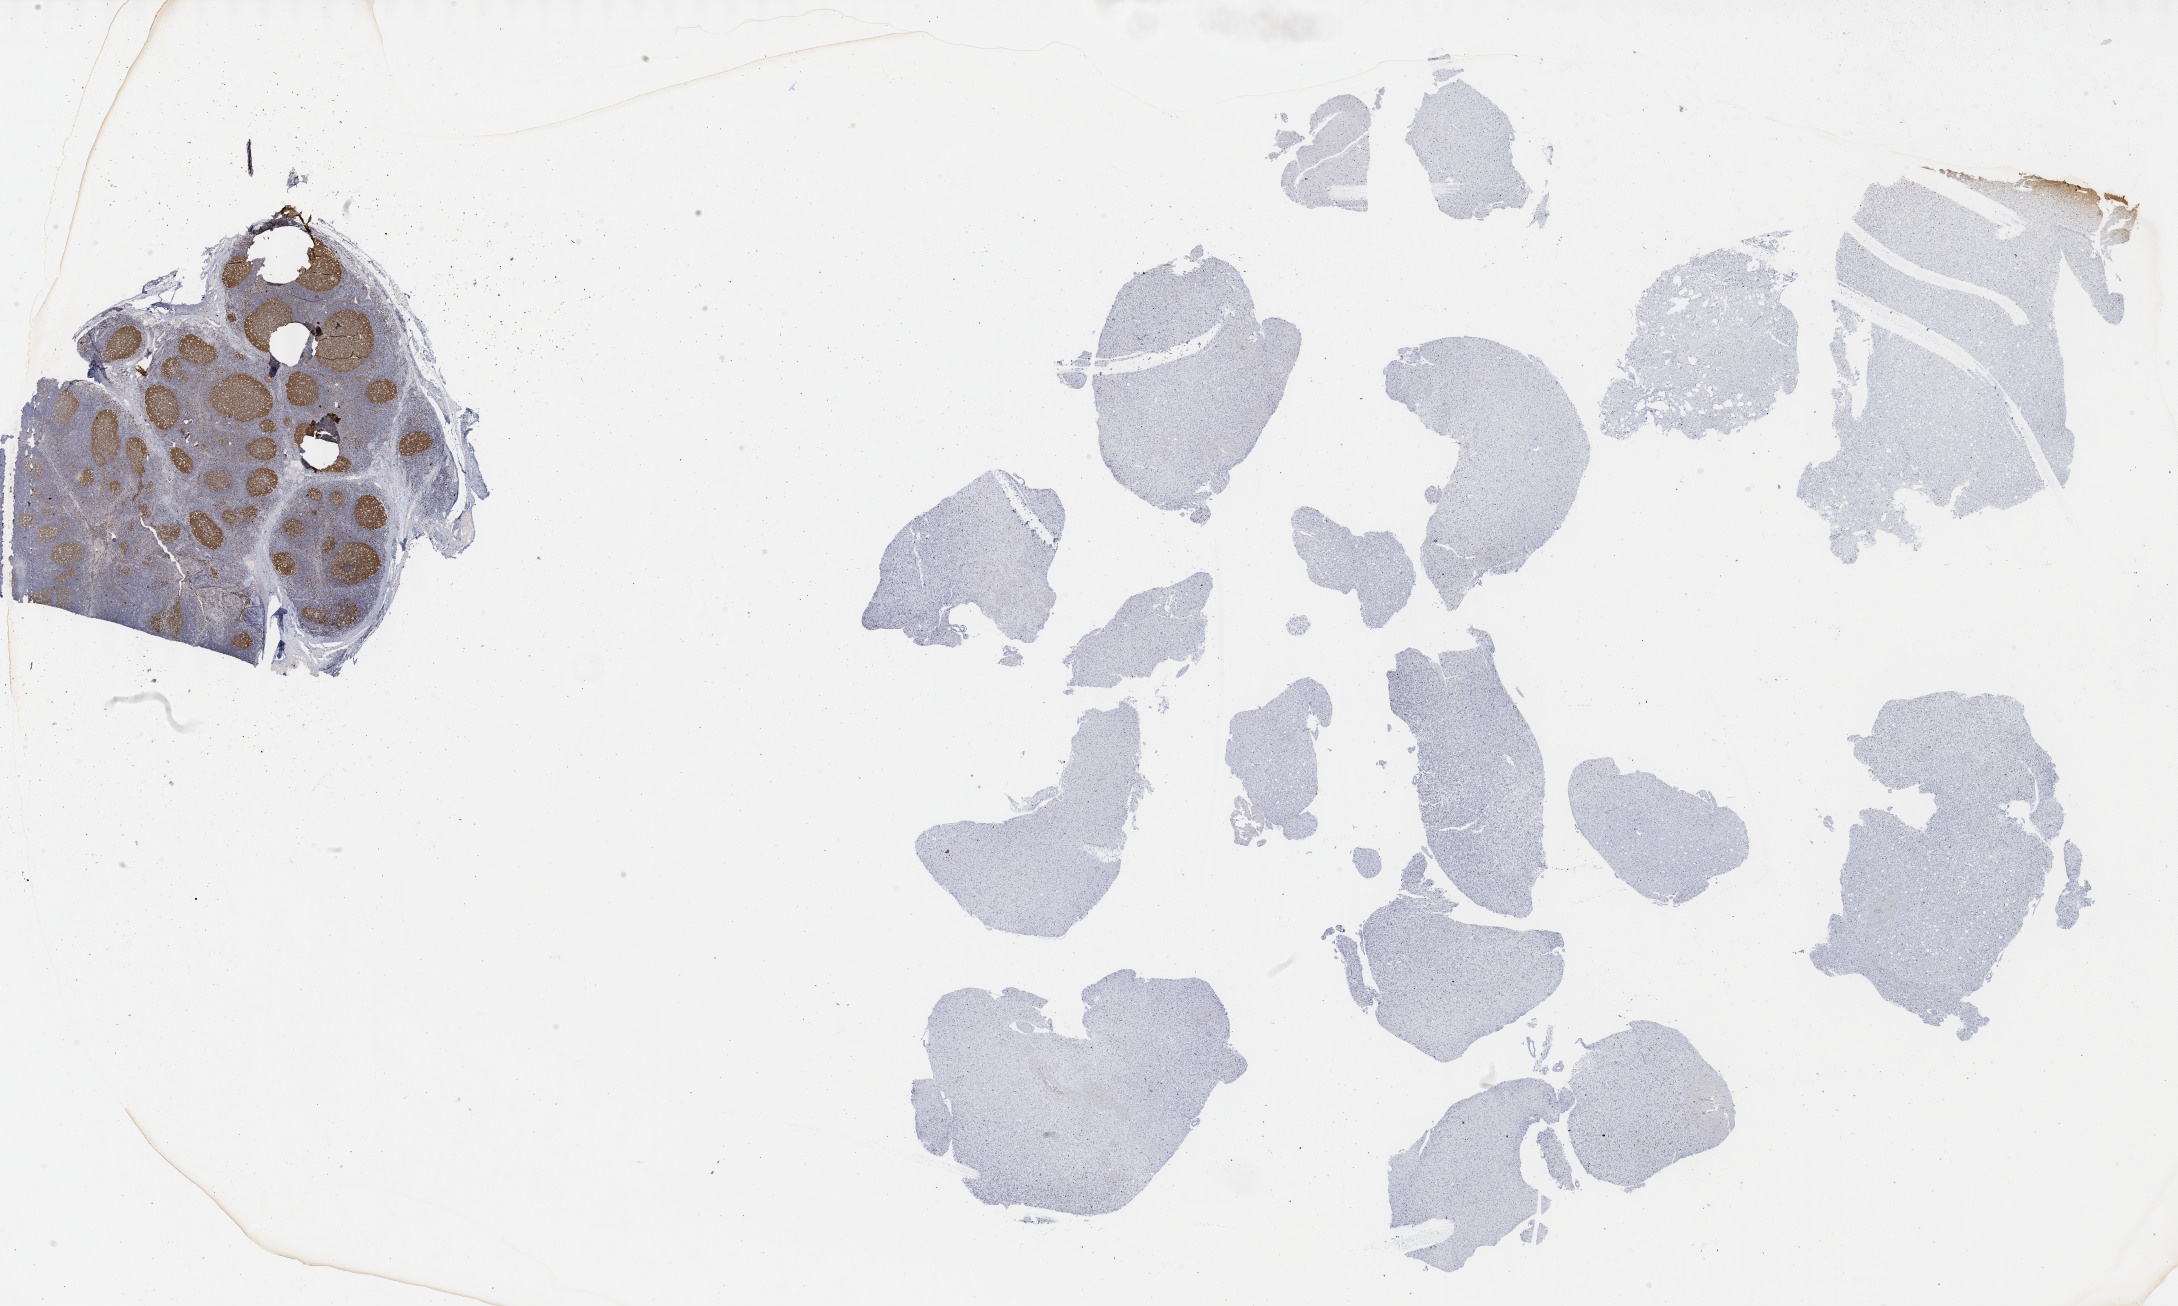
H&E-stained whole-slide image, shown as a low-resolution overview of the whole scanned area (about 35.2 x 21.1 mm, from a 40x scan); formalin-fixed paraffin-embedded (FFPE) diagnostic section; sample: primary tumour, brain. Patient: male, age at initial diagnosis 32 years. Histologic grade: G2 (moderately differentiated).
Histologic diagnosis: Oligodendroglioma, NOS (cerebrum).